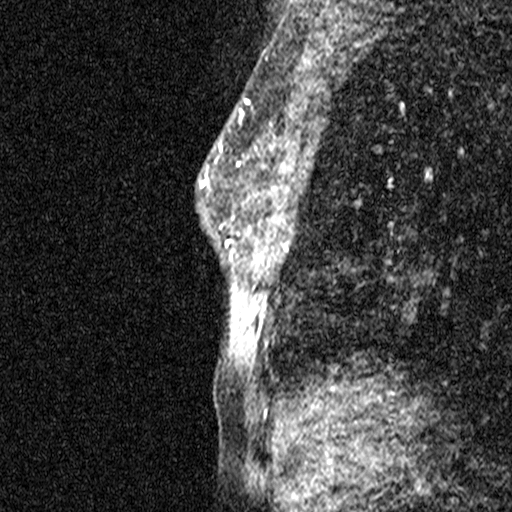
Breast MRI (dynamic contrast-enhanced), one sagittal slice; slice 23 of 44 in the series (ordered by position); dynamic contrast-enhanced study with each time point stored as its own series, time point 2 of 3 at this slice position (early post-contrast, ordered by acquisition time); 1.5 T; TE 4.5 ms, TR 11 ms; 3 mm slice thickness; 512 × 512 image matrix, field of view 200 × 200 mm. Patient: female, 44 years. Case-level facts recorded for this patient, not image findings: setting: breast cancer imaged before/during neoadjuvant chemotherapy; receptor status: HR-positive, HER2-negative.
Outlined on this slice (semi-automatically segmented with operator editing):
- analysis volume of interest (the breast-tissue region the enhancement analysis was run in; not a lesion): bounding box [x1, y1, x2, y2] px = [218, 118, 273, 291]
- tumour enhancement mask (voxels above the 90 % enhancement threshold inside the analysis volume of interest): [221, 119, 241, 166]